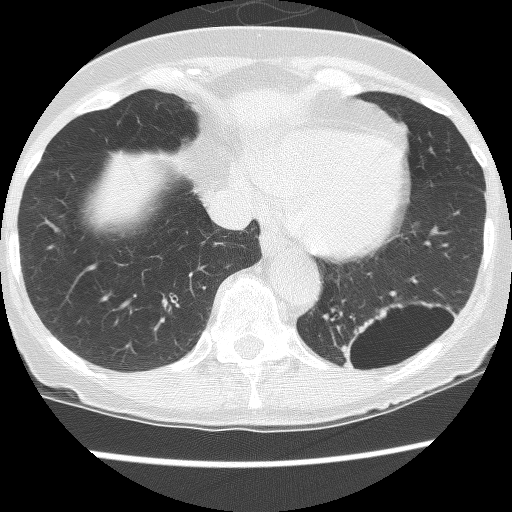
Low-dose screening chest CT, axial slice. Third annual screen. Lung window (W 1500 / L -600 HU). Lung (sharp) reconstruction kernel (BONE). 512 × 512 image matrix. Female, age 61 years at enrolment. Current smoker at enrolment.
Expert-annotated lung lesion, bounding box [x1, y1, x2, y2] px = [334, 293, 444, 387]. The screening reader recorded 2 non-calcified nodules or masses ≥4 mm on this exam (left lower lobe, left lower lobe); which of them this box marks is not recorded. Participant outcome: lung cancer diagnosed 166 days after this screen — non-small cell carcinoma, left lower lobe, poorly differentiated (G3), stage IB (AJCC 6th edition), 100 mm at pathology.